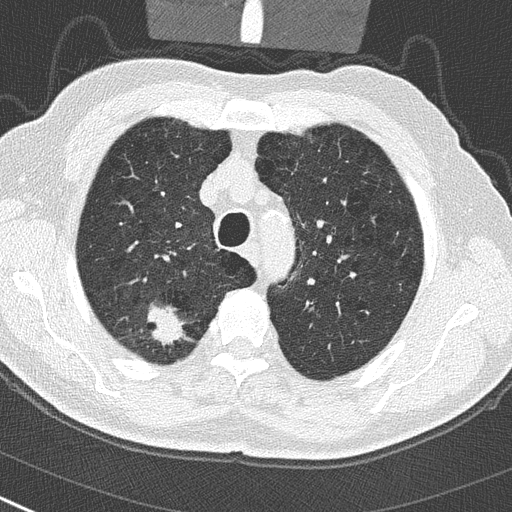
Low-dose screening chest CT, one axial slice; slice 226 of 290 in the series (ordered by position); reconstruction kernel B50f; 120 kVp; lung window (W 1500 / L -600 HU); 2 mm slice thickness; 512 × 512 image matrix, field of view 300 × 300 mm.
Structures marked on this image (expert manual segmentation):
- lesion 1 (tumor, upper lobe of right lung): bounding box <147,305,186,347> (left, top, right, bottom; pixels)